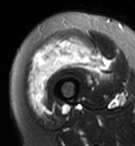
MRI of an extremity soft-tissue mass, one axial slice. Position 27 of 95 along the scan axis. T2-weighted fat-saturated. MR volume resampled by the dataset authors to the PET/CT grid (not the native acquisition matrix). 3.27 mm slice thickness. 135 × 146 image matrix, field of view 132 × 143 mm. Female patient. Case-level facts recorded for this patient, not image findings: histological type: pleiomorphic undifferentiated sarcoma; grade: high; site of the primary tumour: right quadricep.
Structures marked on this image (expert contour drawn on MRI and transferred to this co-registered scan by the dataset authors):
- gross tumour volume including surrounding oedema: box from (x=28, y=38) to (x=106, y=112) px